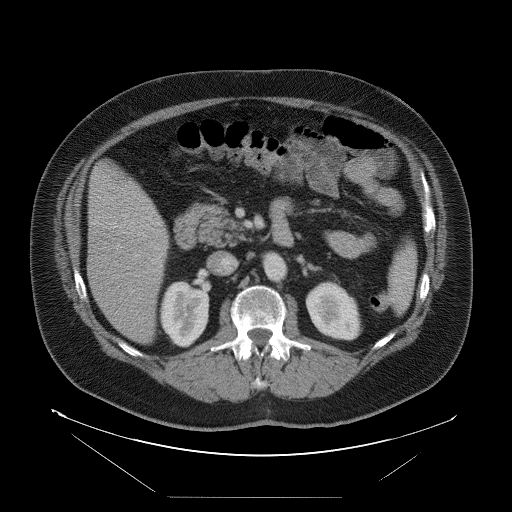
Contrast-enhanced abdominal CT, one axial slice. Position 39 of 114 along the scan axis. Intravenous contrast given. Soft-tissue window (W 400 / L 40 HU). 512 × 512 image matrix, field of view 500 × 500 mm. Male patient, age 61 years. From the clinical record (not read from this slice): diagnosis: colorectal cancer liver metastases, imaged before liver resection.
Annotated regions visible in this slice (expert manual segmentation):
- liver: bounding box [x1, y1, x2, y2] px = [89, 164, 169, 344]